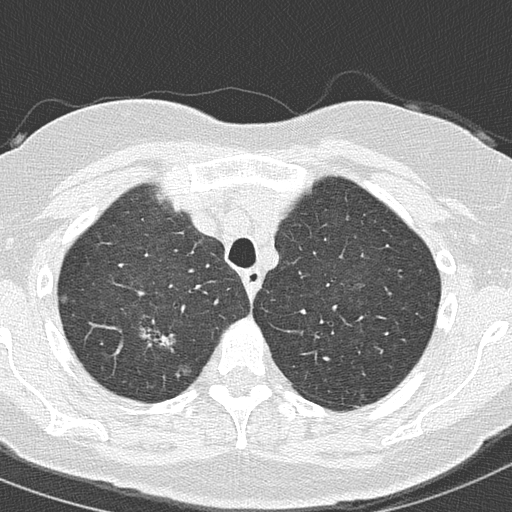
Chest CT (low-dose screening protocol), one axial image, second annual screen, lung window (W 1500 / L -600 HU), 2 mm slice thickness, lung (sharp) reconstruction kernel (B50f), 120 kVp, slice 34 of 157 in the series, 512 × 512 image matrix, field of view 280 × 280 mm. Female, age 61 years at enrolment.
Expert-annotated lung lesion, bounding box <144,316,186,357> (left, top, right, bottom; pixels). Reader record for this screening exam (exam-level; its link to the box is not recorded): non-calcified nodule or mass ≥4 mm, right upper lobe, 15 × 10 mm, spiculated (stellate) margins, ground glass attenuation, pre-existing on the prior screen: yes; interval growth: yes. Later outcome: lung cancer diagnosed 91 days after this screen — adenocarcinoma, NOS, right upper lobe, moderately differentiated (G2), stage IA (AJCC 6th edition), 20 mm at pathology.